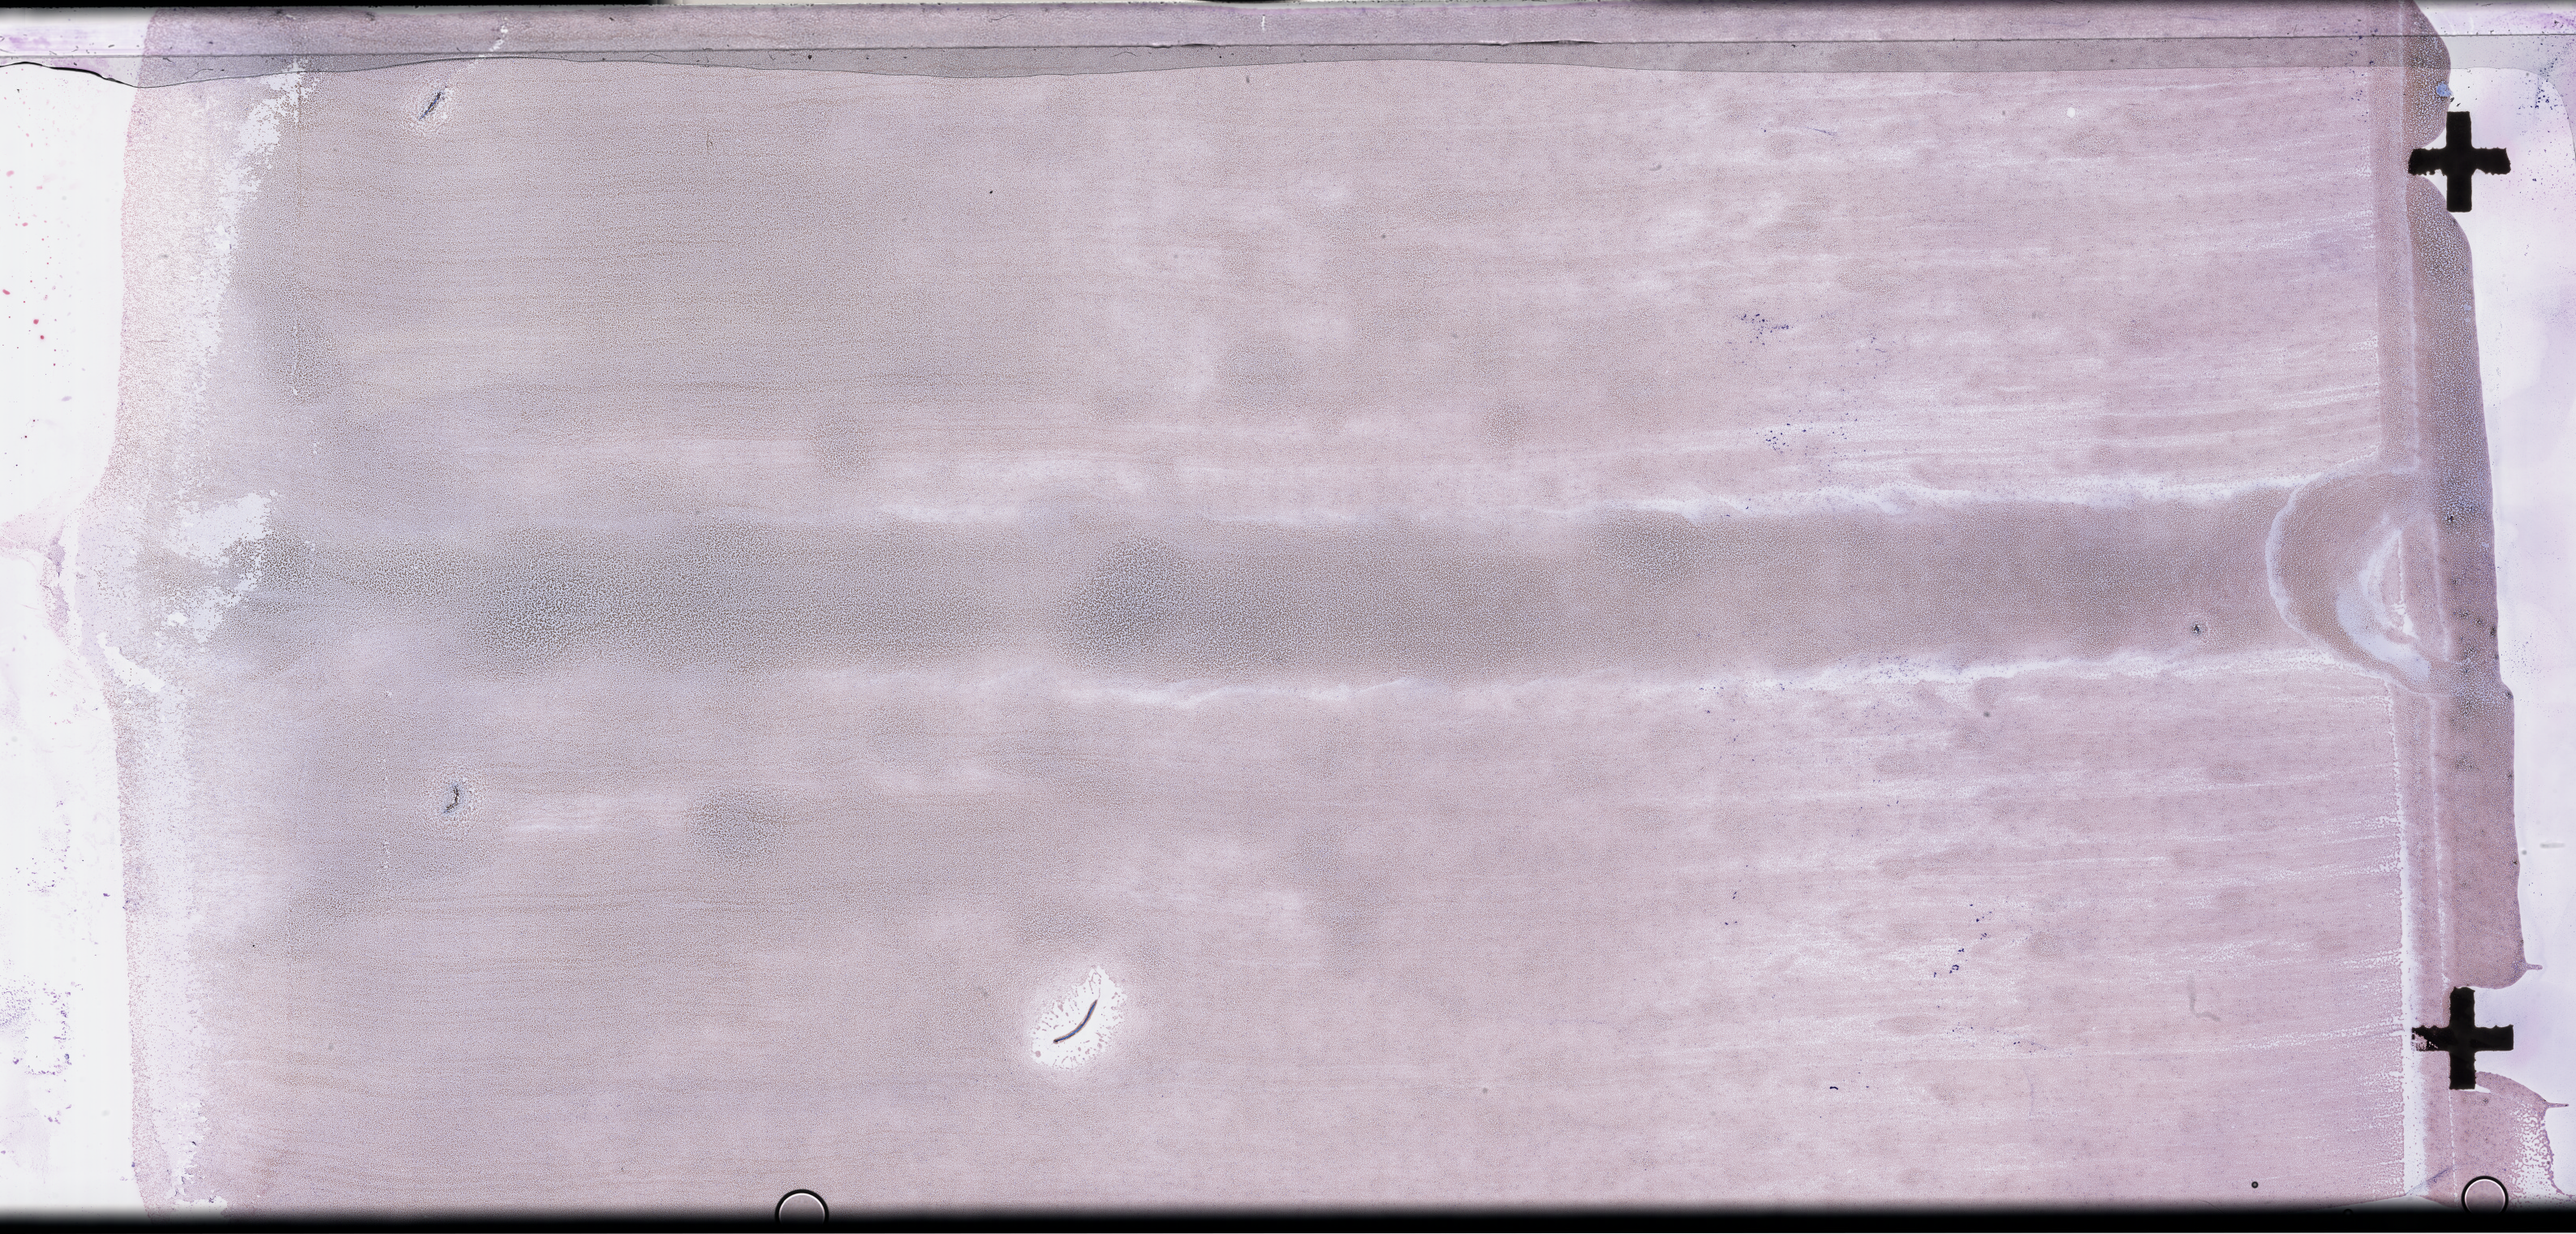
Wright-Giemsa-stained whole blood smear, whole-slide image, whole scanned area (about 51.3 x 24.6 mm) shown as a low-resolution overview; EDTA-anticoagulated smear; specimen time point: collected on treatment. Patient sex: female.
• from a patient with: Plasma Cell Myeloma